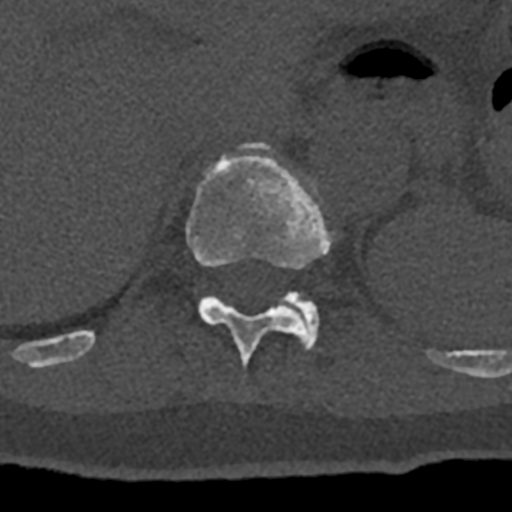
CT including the spine, one axial slice. Position 537 of 797 along the scan axis. Reconstruction kernel Br40s/3. Bone window (W 1800 / L 400 HU). 512 × 512 image matrix, field of view 160 × 160 mm. Male patient, age 74 years. Case-level facts recorded for this patient, not image findings: primary cancer: renal.
Annotated regions visible in this slice (semi-automatic segmentation, software-assisted and operator-edited):
- T11 vertebra: bounding box [x1, y1, x2, y2] px = [70, 142, 432, 367]
- T12 vertebra: [281, 291, 319, 348]